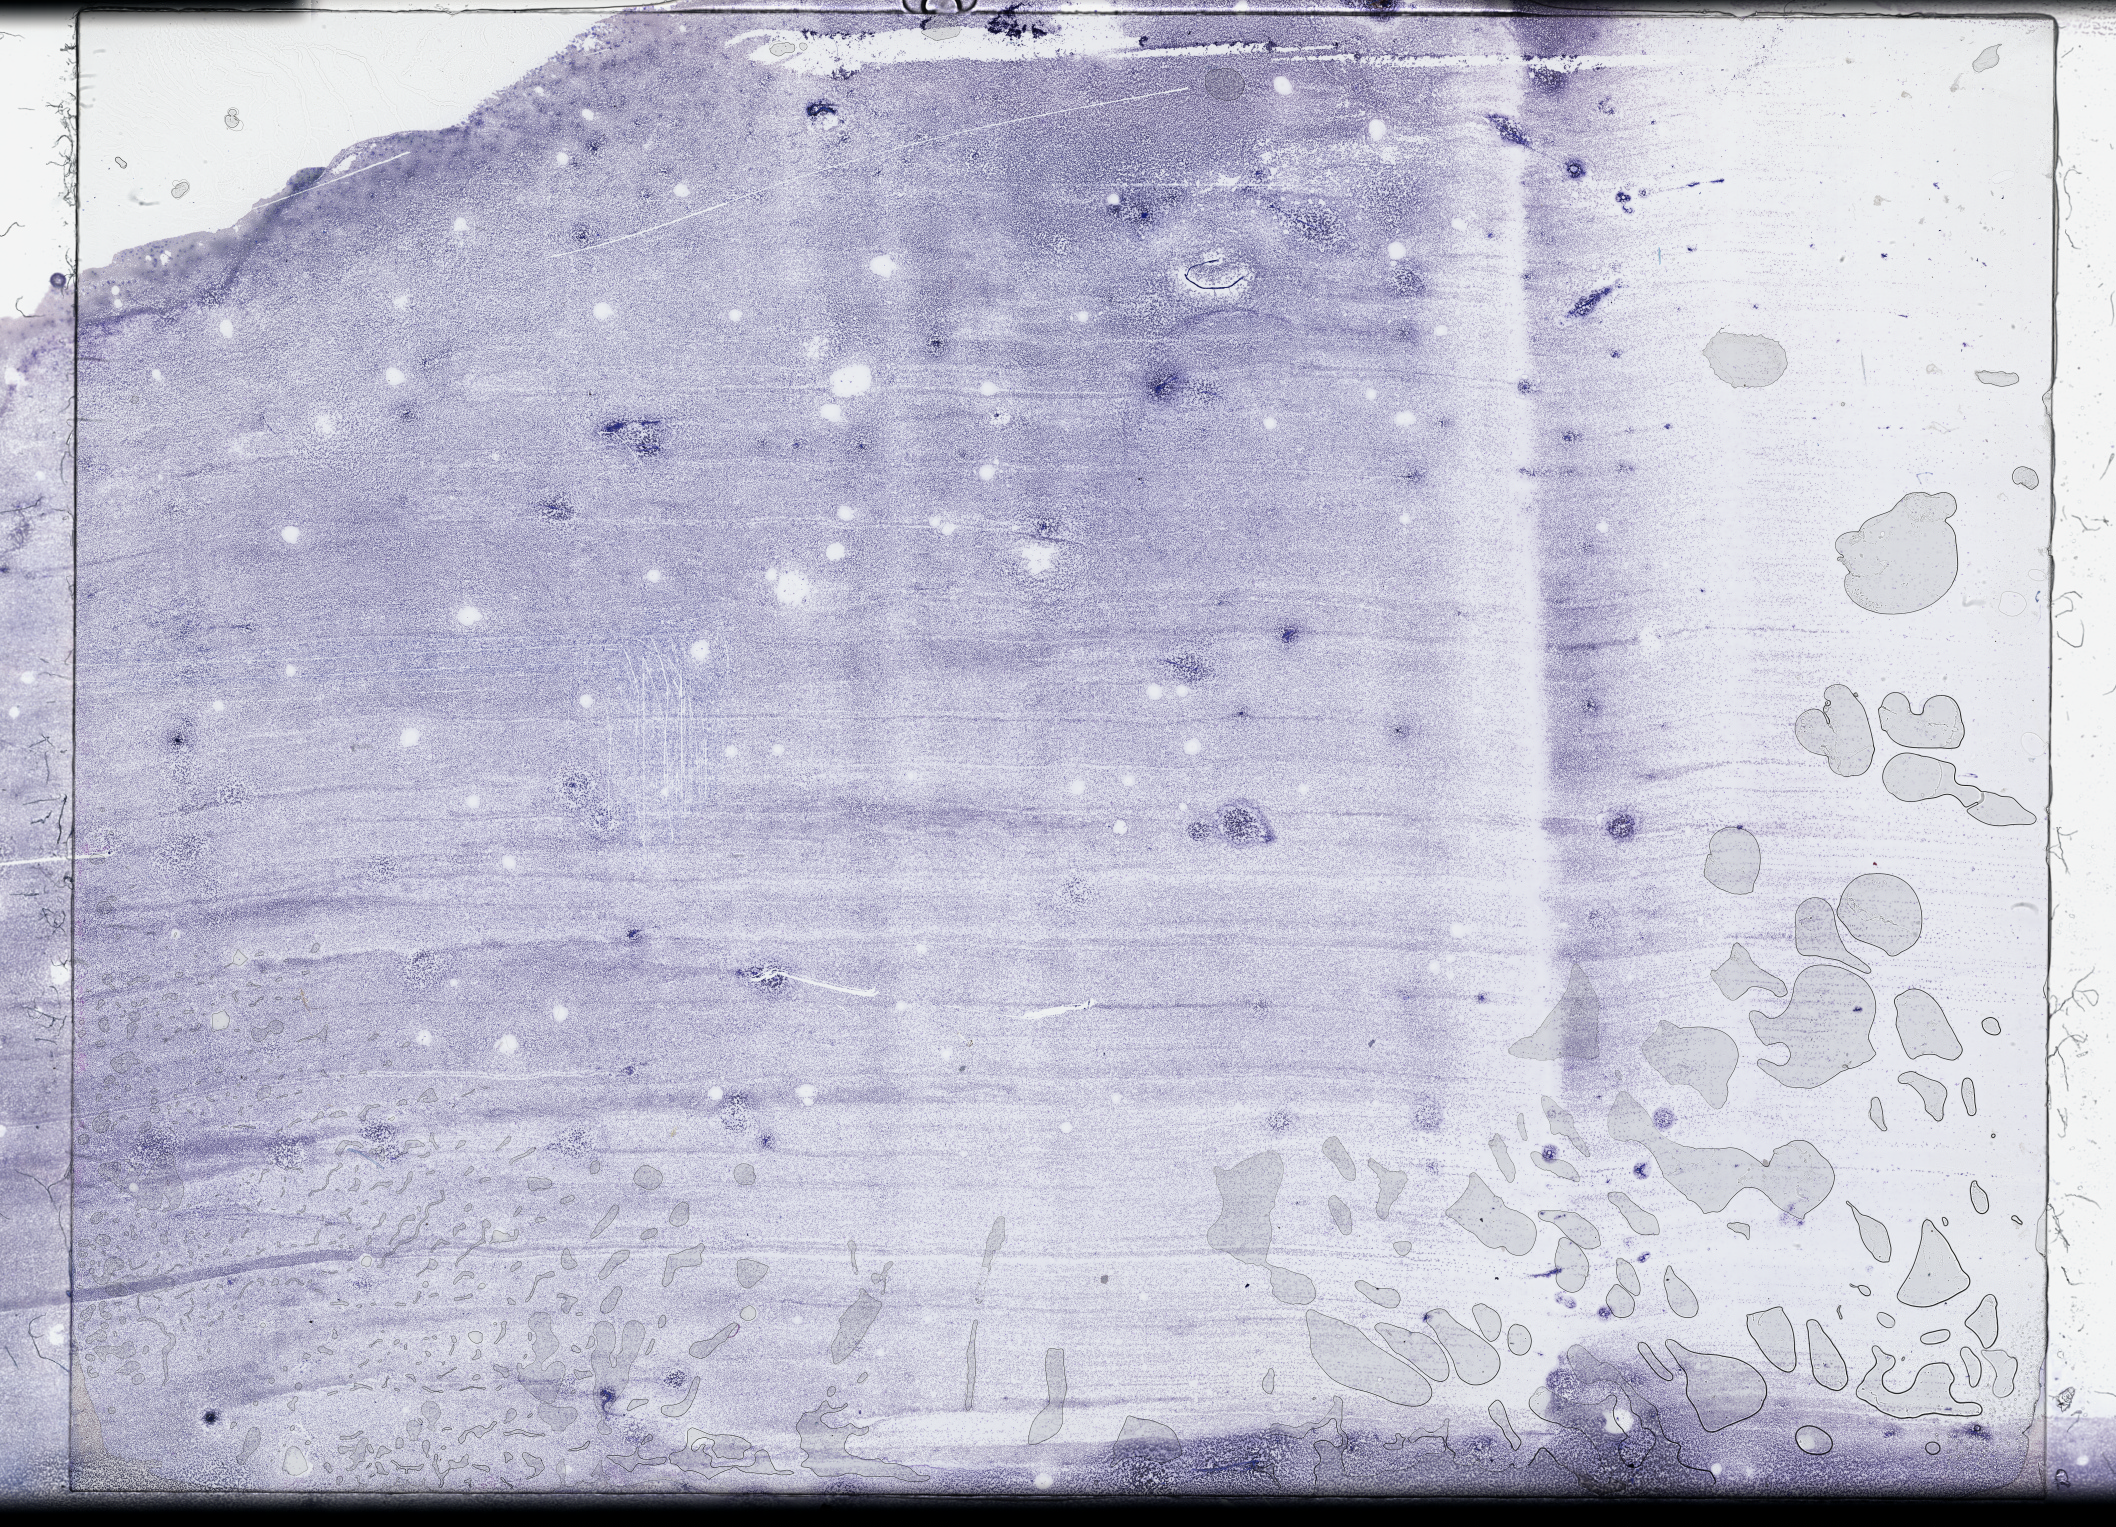
Whole-slide histology image, H&E-stained, a low-resolution overview of the entire scanned area, about 34.2 x 24.7 mm (slide scanned at 40x), bone marrow (leukaemic) sample. 71-year-old male patient. Blasts: 50%.
* diagnosis: Acute Myeloid Leukemia
* FAB classification: M2